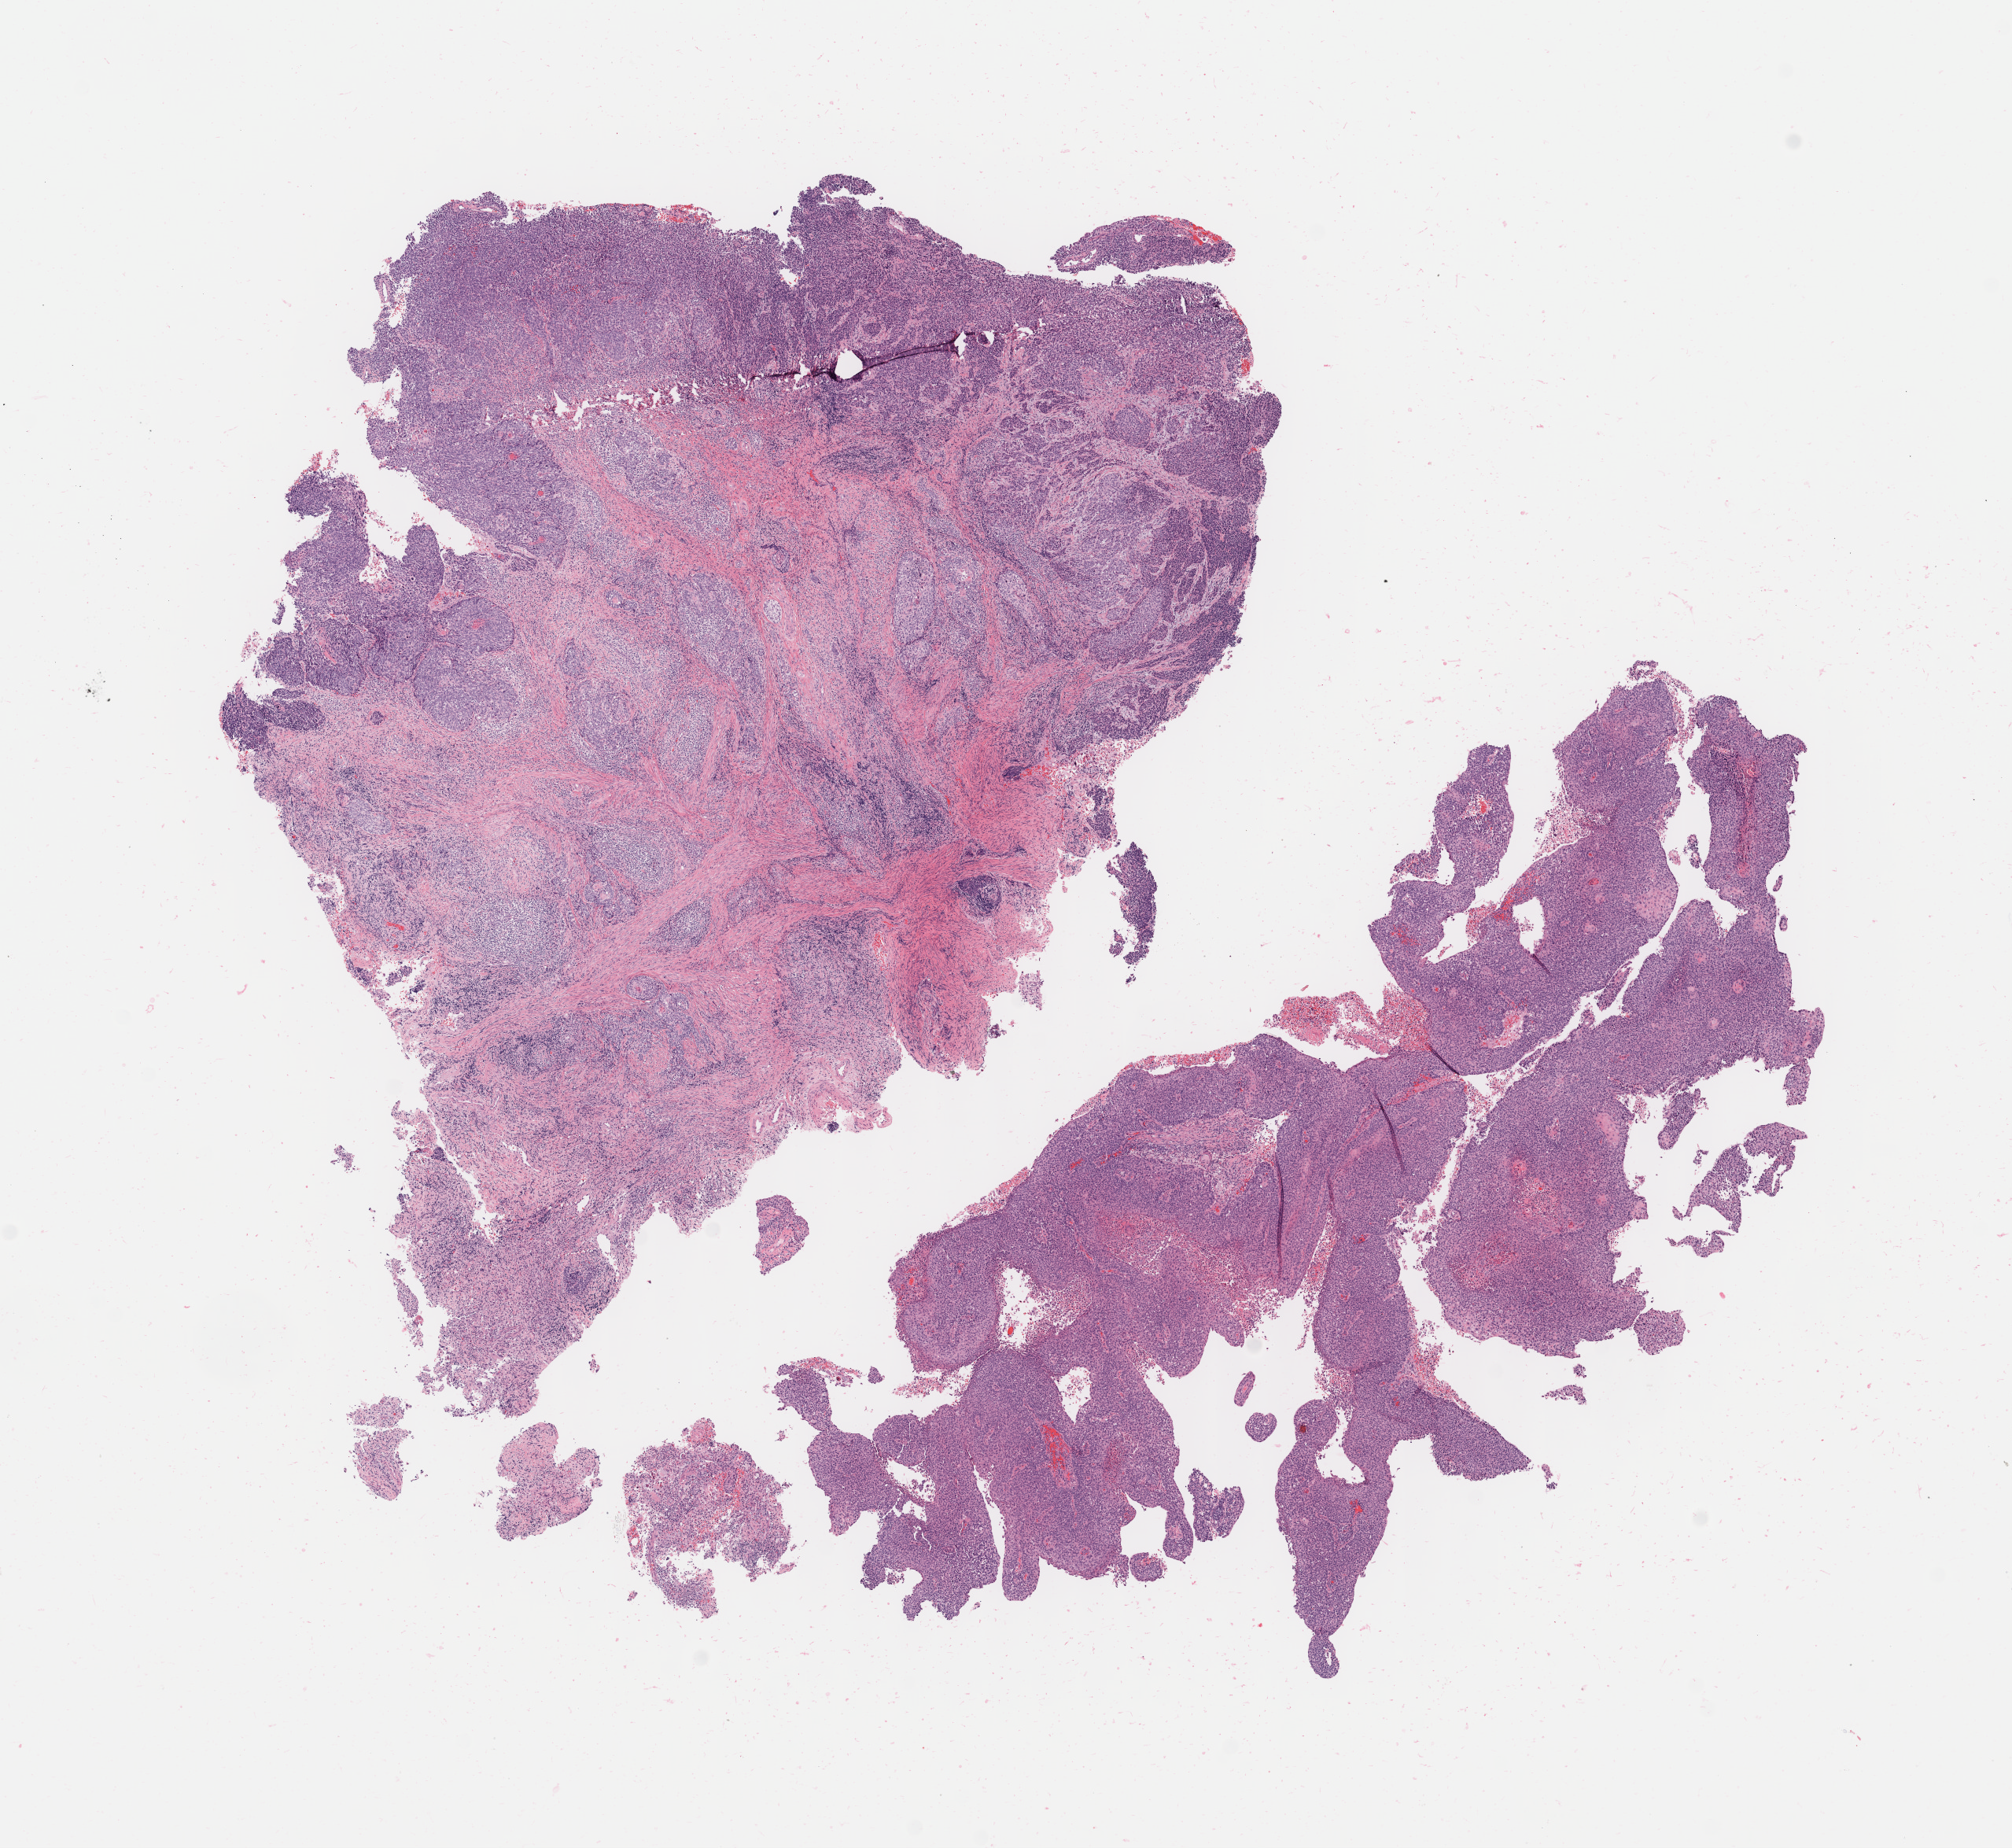
Whole-slide image, haematoxylin and eosin stain, whole scanned area (about 10.2 x 9.3 mm) shown as a low-resolution overview; tumor tissue; anatomic site: cervix. Patient female; aged 49.
Diagnosis: Squamous cell carcinoma, keratinizing, NOS.